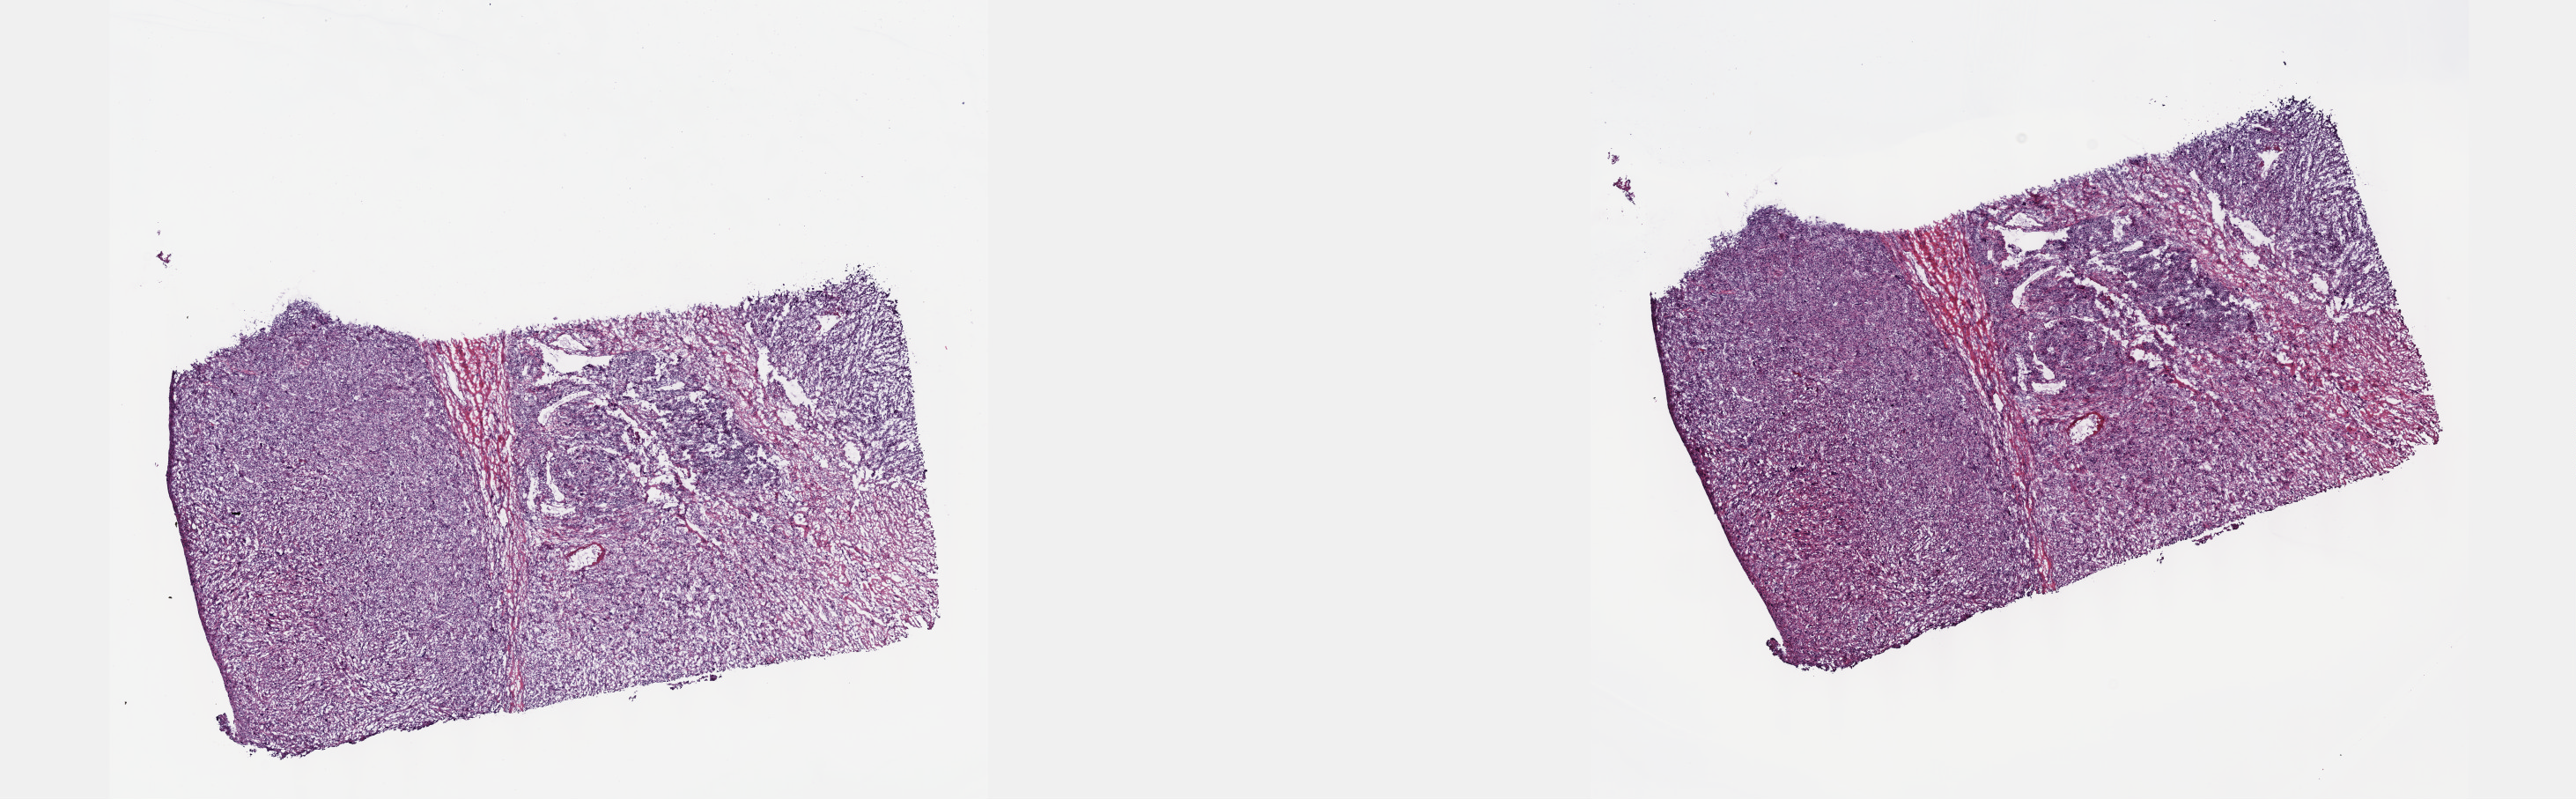
Digitized H&E-stained tissue section (whole slide) — whole scanned area (about 23.6 x 7.3 mm) shown as a low-resolution overview, frozen section from the top of the tissue portion, primary tumour sample from the pancreas. Female, age 58 years at initial diagnosis. Histologic grade: G4 (undifferentiated). Pathologist review of this section (percent, as recorded): tumour cells 100%, tumour nuclei 75%, normal cells 0%, stromal cells 0%, necrosis 0%. Inflammatory infiltration, as recorded: lymphocyte infiltration 3%, monocyte infiltration 0%, neutrophil infiltration 0%.
• AJCC pathologic stage: IIB (7th edition)
• lymph nodes positive (case pathology): 1 of 22 examined
• histologic diagnosis: Carcinoma, undifferentiated, NOS (head of pancreas)